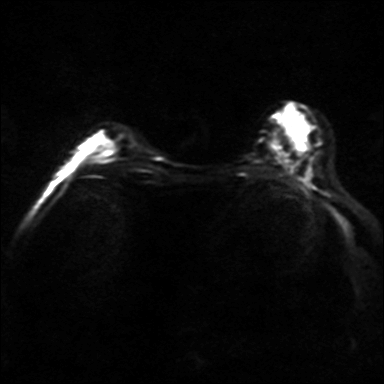
Breast MRI, one axial slice. Position 14 of 36 along the scan axis. Diffusion-weighted series; image 2 of 4 stored at this slice position (different b-values; order by instance number). 3 T. 4 mm slice thickness. 384 × 384 image matrix. Female patient.
Outlined on this slice (outlined manually by an expert reader):
- tumour on diffusion-weighted imaging: box from (x=104, y=140) to (x=116, y=150) px